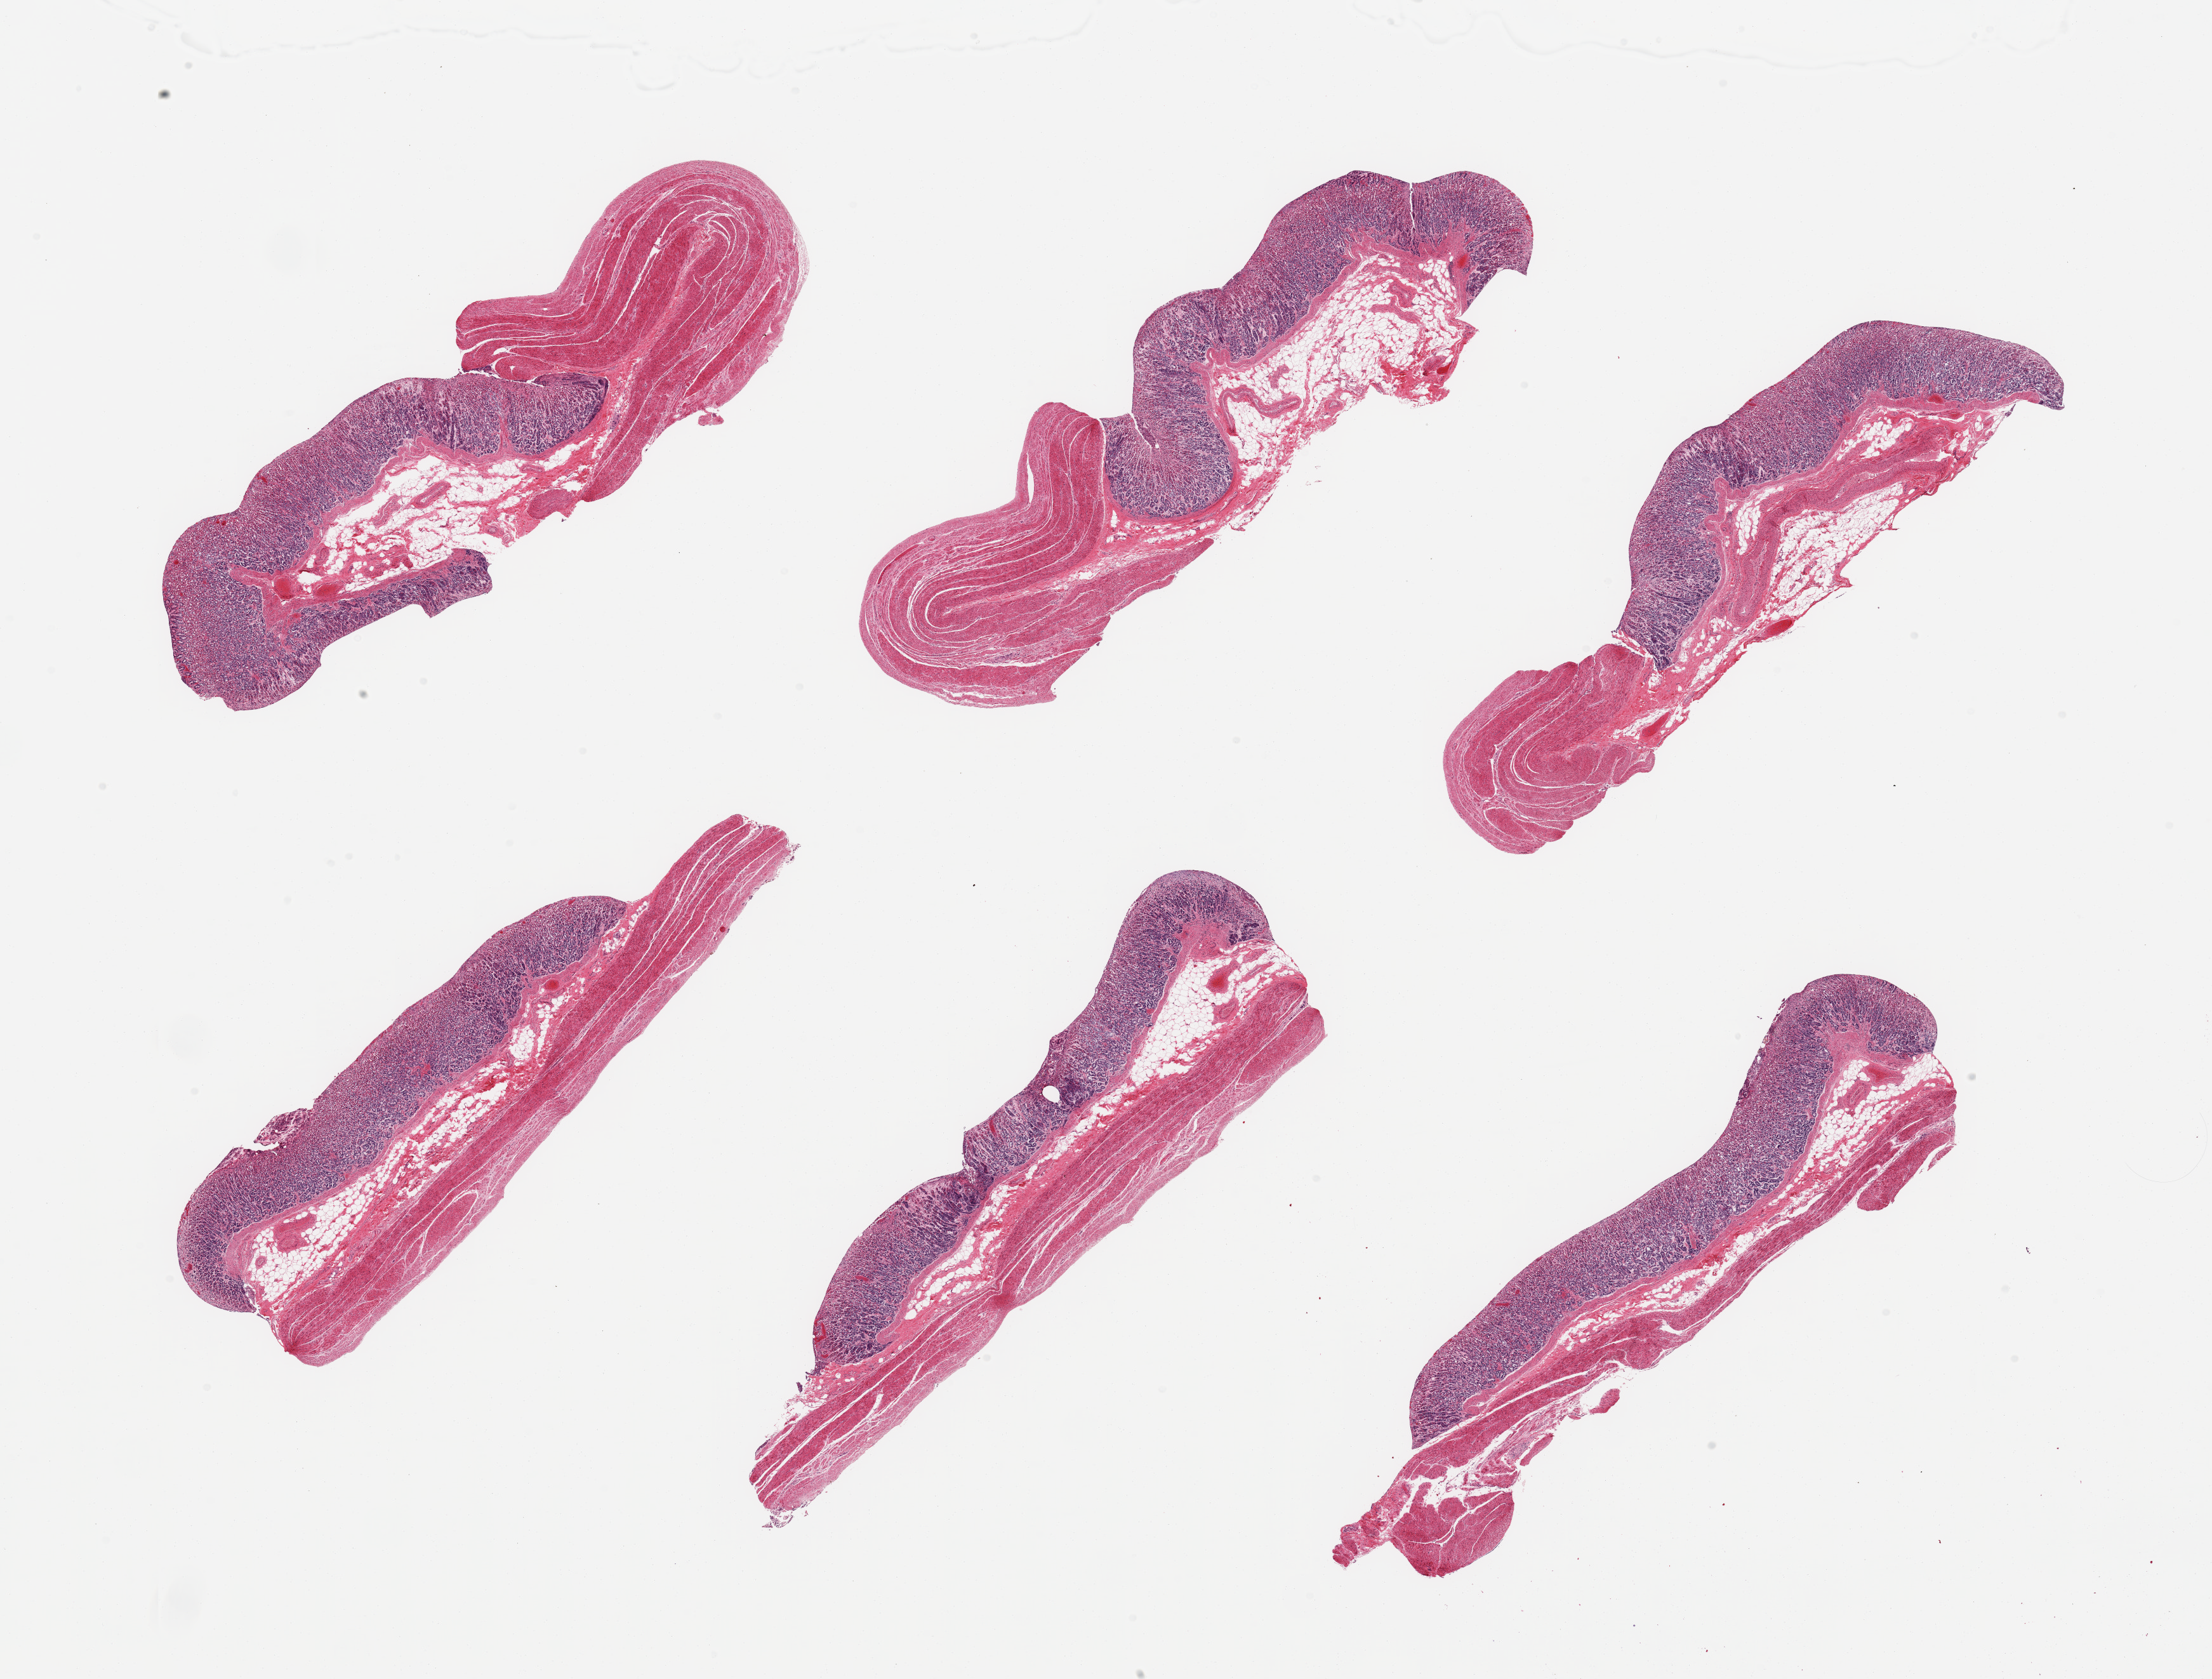
Digitized haematoxylin and eosin-stained section — shown as a low-resolution overview of the whole scanned area (about 27.6 x 20.9 mm, slide scanned at 20x), PAXgene-fixed, paraffin-embedded tissue, sampled site (target tissue): stomach, tissue donor sample. Donor sex: male.
Review note (as recorded): 6 pieces, target mucosa up tp ~1mm thick, ~50% thickness, moderately advanced autolysis.